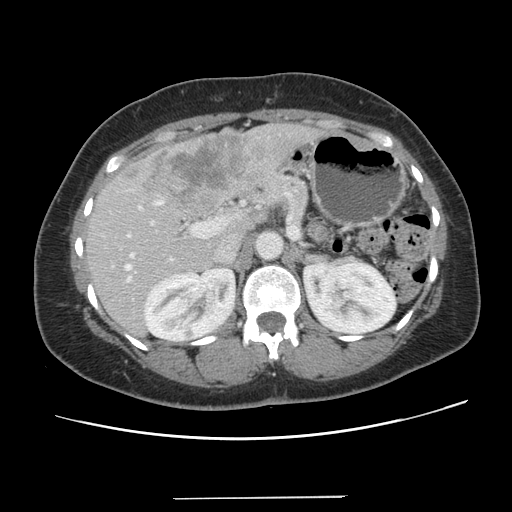
Contrast-enhanced abdominal CT, one axial slice; slice 73 of 141 in the series (ordered by position); intravenous contrast given; soft-tissue window (W 400 / L 40 HU); 2.5 mm slice thickness; 512 × 512 image matrix. Female patient, age 53 years. From the clinical record (not read from this slice): diagnosis: colorectal cancer liver metastases, imaged before liver resection; multiple liver metastases: no; largest metastasis: 14.5 cm.
Outlined on this slice (outlined manually by an expert reader):
- hepatic veins: bounding box (x1, y1, x2, y2) in pixels: (125, 253, 133, 280)
- liver: (87, 122, 318, 335)
- planned liver remnant (the part of the liver to remain after resection): (88, 206, 252, 335)
- portal vein (with intrahepatic branches): (127, 200, 230, 238)
- liver metastasis: (142, 133, 254, 203)